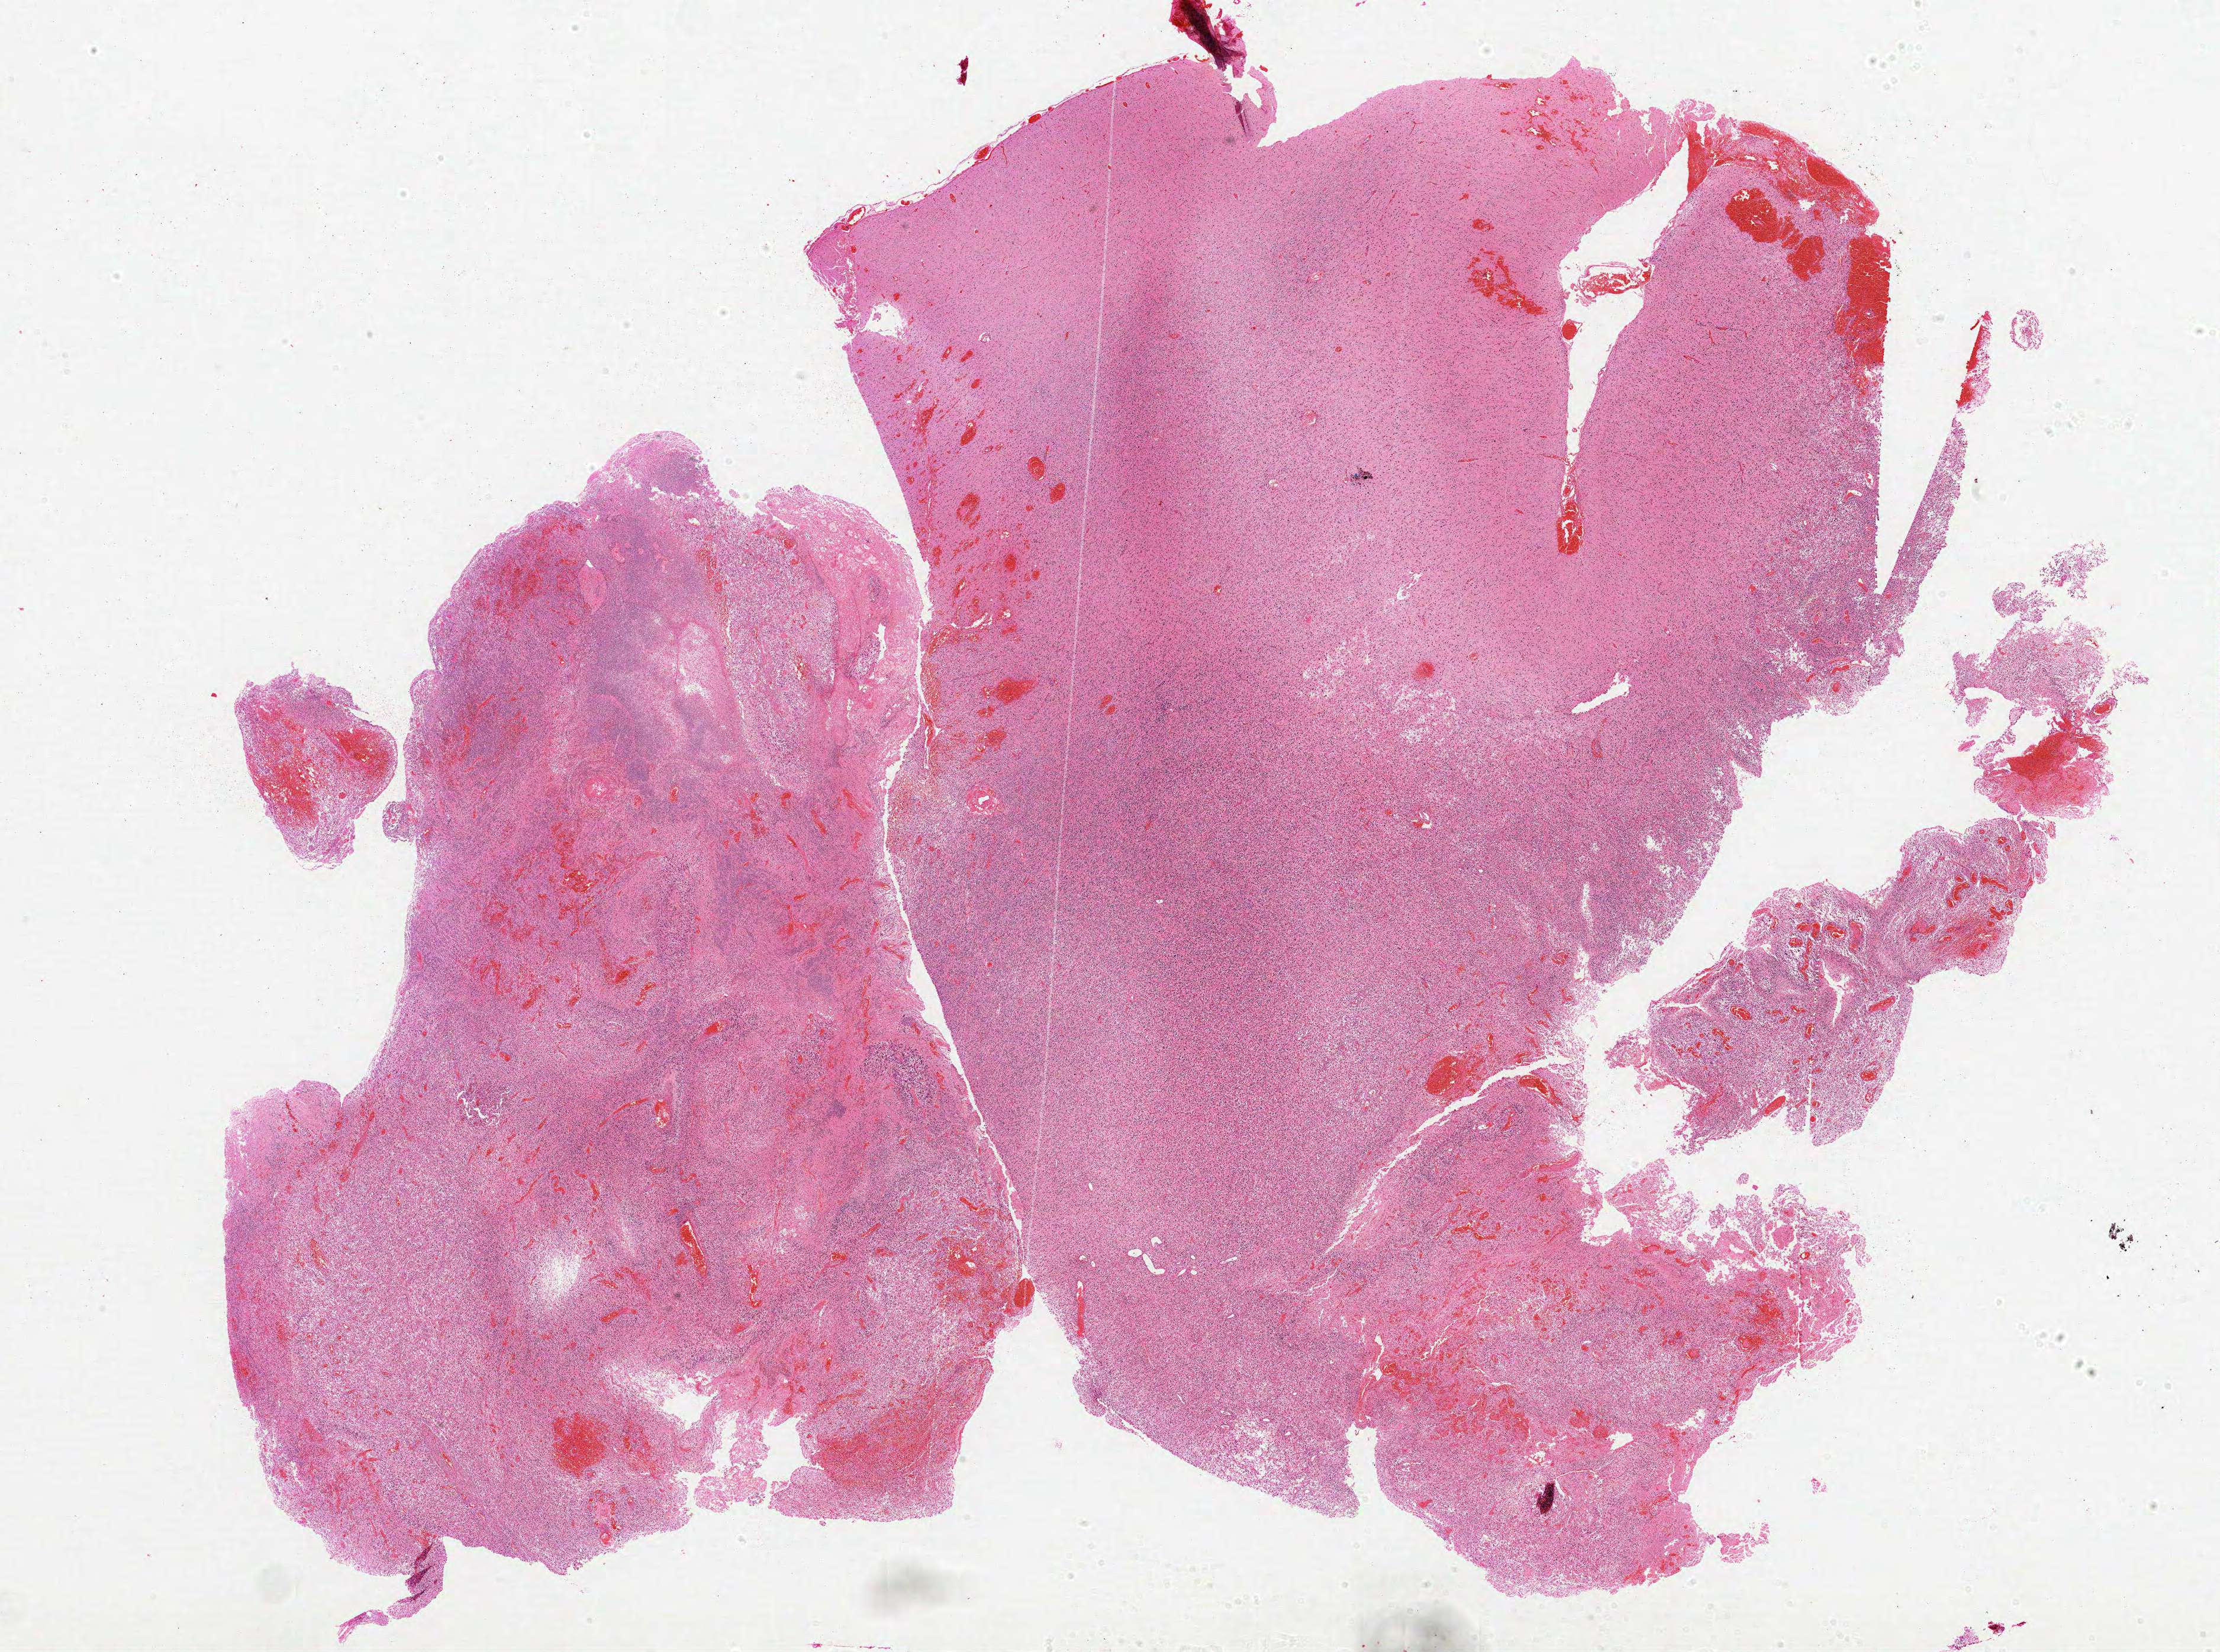
Whole-slide histology image, Hematoxylin and eosin (H&E) stained, whole scanned area (about 30.0 x 22.3 mm, from a 20x scan) shown as a low-resolution overview, formalin-fixed paraffin-embedded (FFPE) diagnostic section, brain, primary tumour sample. Female patient; age at initial diagnosis 53 years.
• diagnosis: Glioblastoma